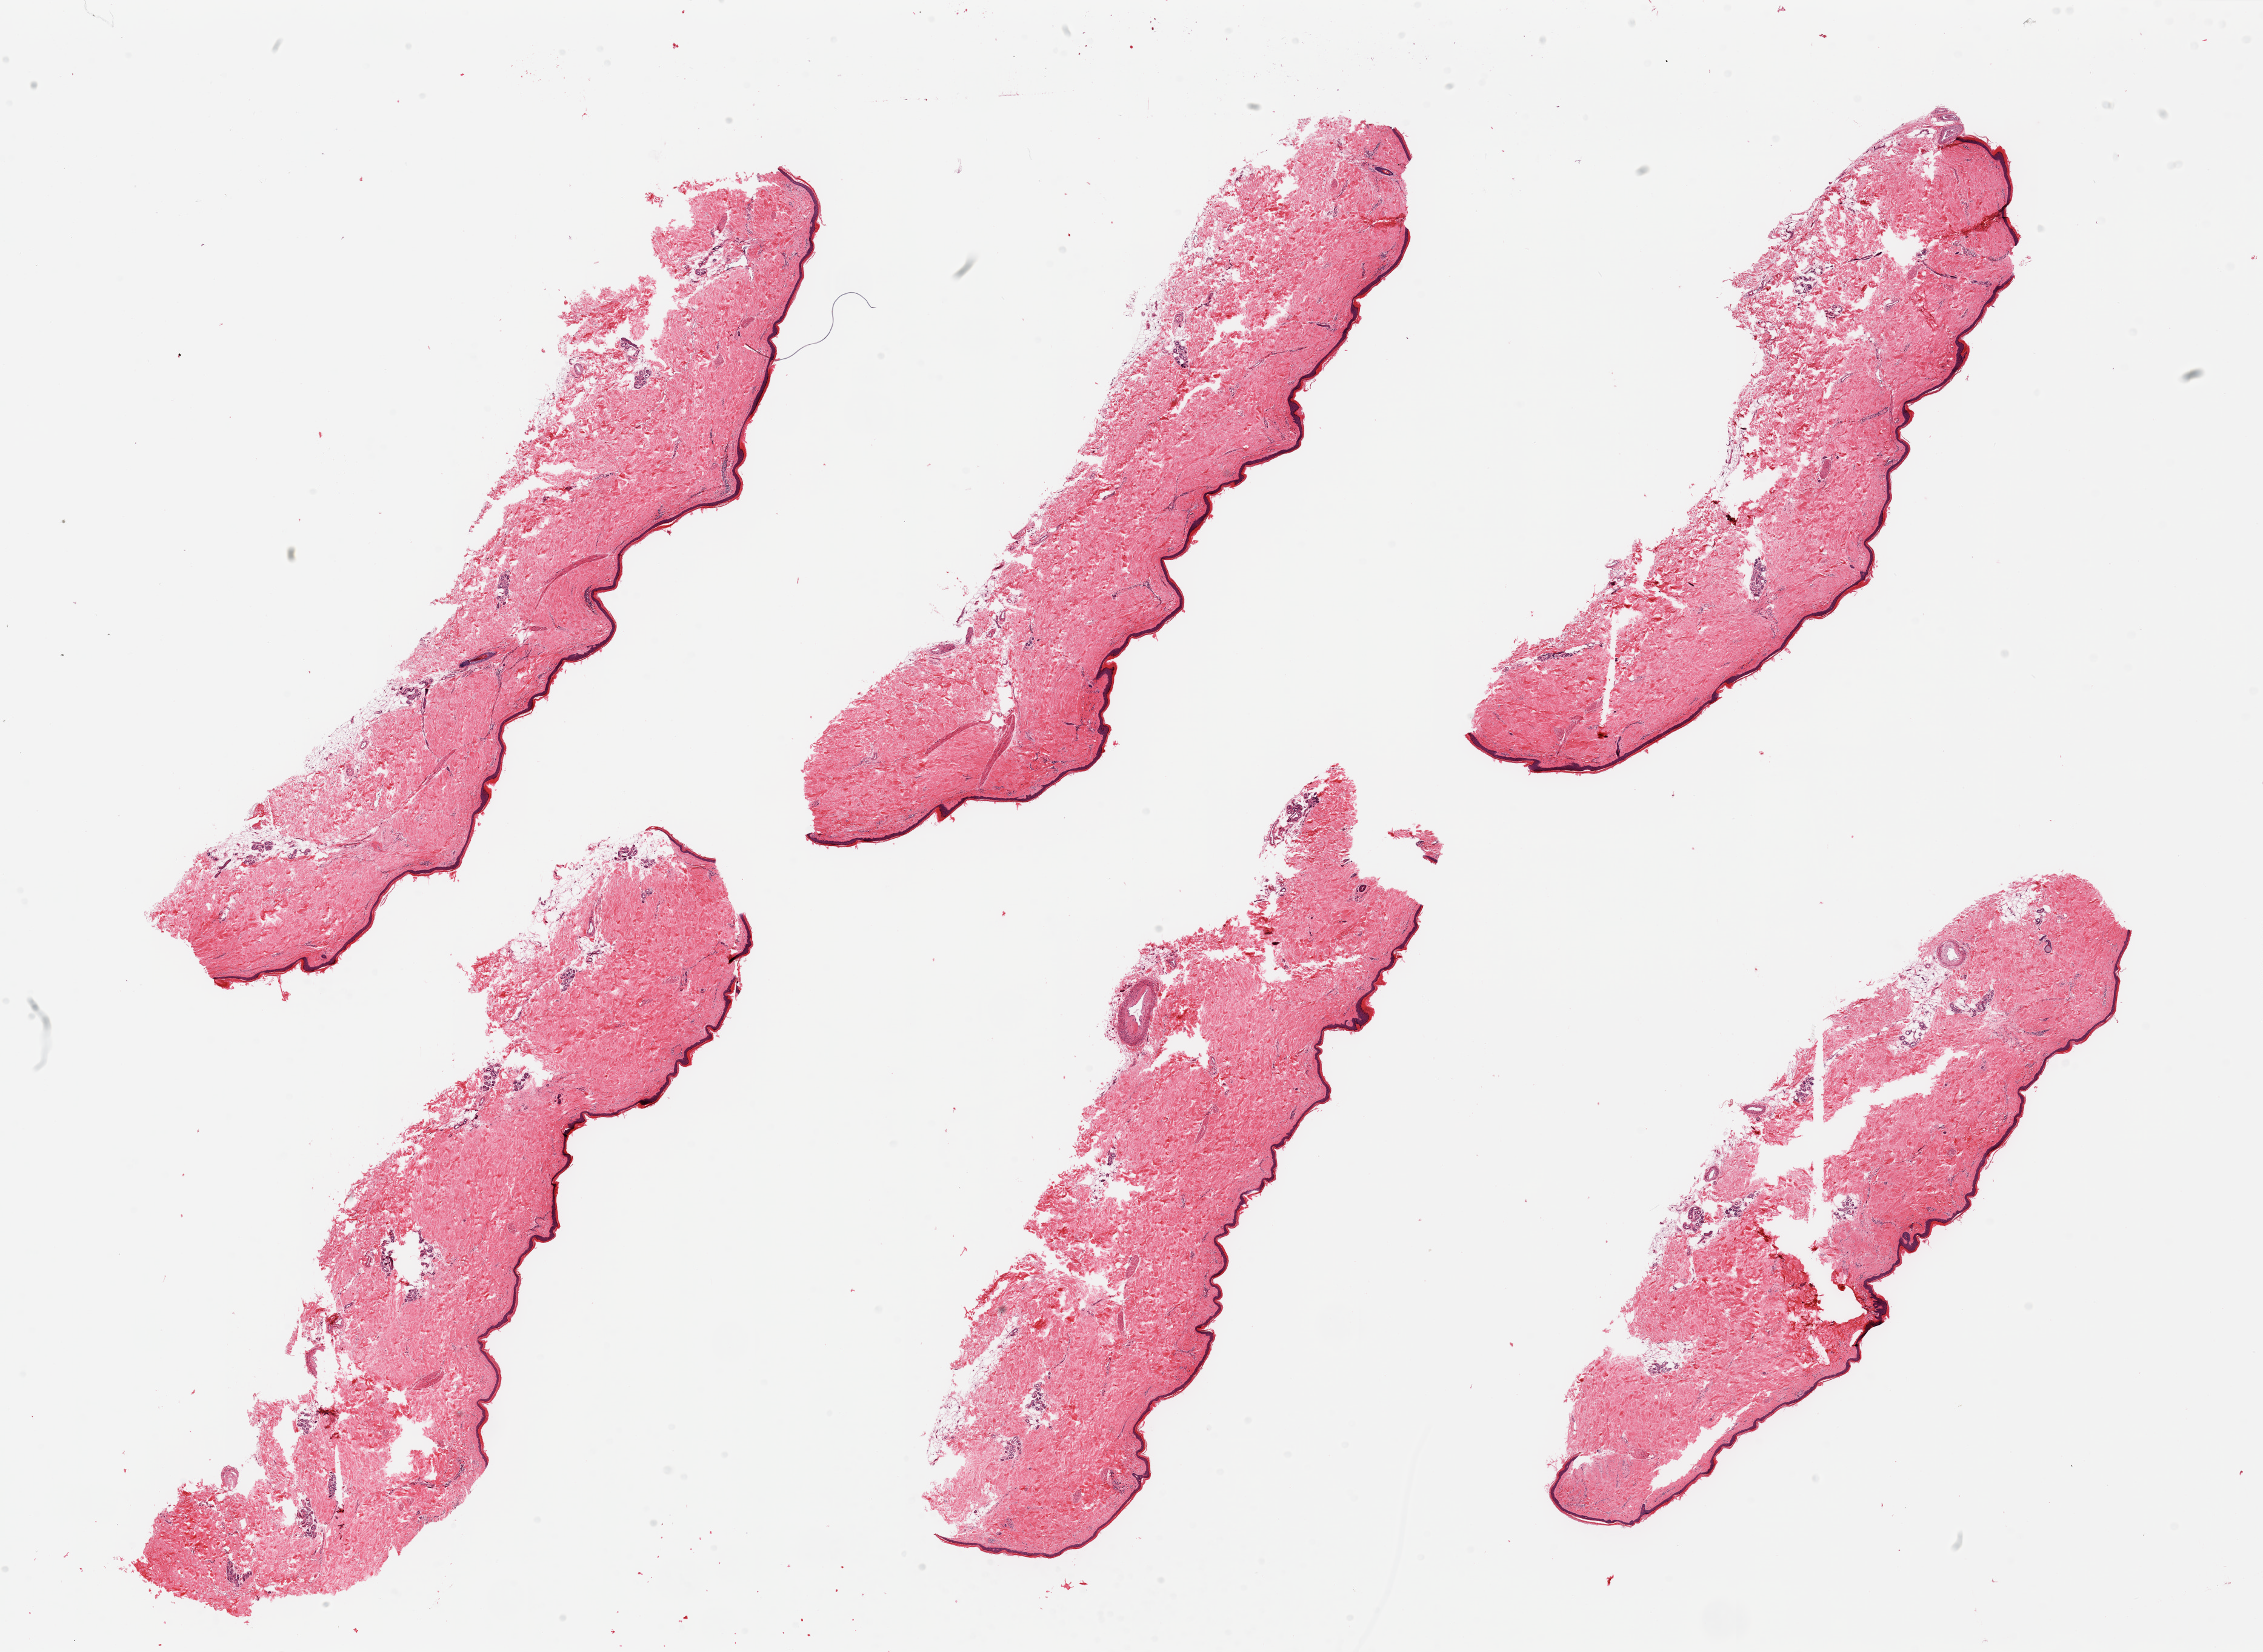
Whole-slide image, H&E stain — low-resolution overview of the scanned area, about 29.5 x 21.6 mm (acquisition: 20x scan). PAXgene-fixed, paraffin-embedded tissue. Sampled site (target tissue): skin of lower leg. Donor tissue sample. Donor sex: male.
Pathologist's review note for this sample: 6 pieces; ~36um thick epidermis; minimal periadnexal fat; numerous empty spaces (fixation related?).